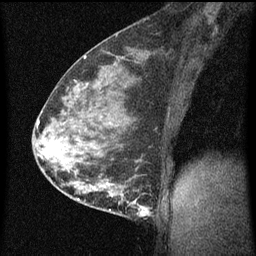
Breast MRI (dynamic contrast-enhanced), one sagittal slice; dynamic contrast-enhanced series, image 2 of 3 at this slice position (ordered by acquisition); 1.5 T; TE 4.2 ms, TR 8 ms; 2 mm slice thickness; 256 × 256 image matrix. Female patient, age 35 years.
Annotated regions visible in this slice (semi-automatic segmentation, software-assisted and operator-edited):
- analysis volume of interest (the breast-tissue region the enhancement analysis was run in; not a lesion): box from (x=110, y=178) to (x=155, y=219) px
- tumour enhancement mask (voxels above the 70 % enhancement threshold inside the analysis volume of interest): (x=110, y=180)–(x=153, y=217)